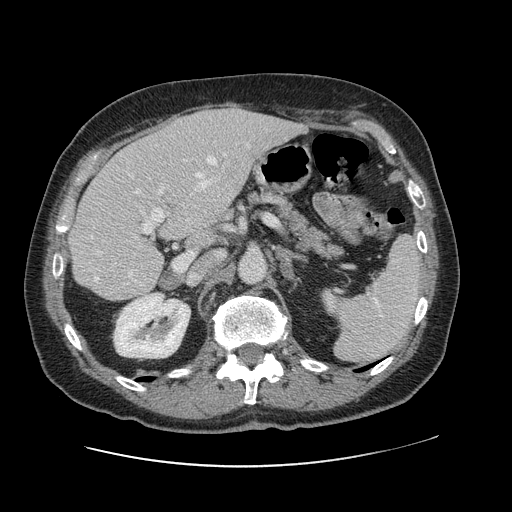
Contrast-enhanced abdominal CT, one axial slice; slice 64 of 138 in the series (ordered by position); 120 kVp; intravenous contrast given; soft-tissue window (W 400 / L 40 HU); 512 × 512 image matrix, field of view 402 × 402 mm. Male patient, age 71 years. From the clinical record (not read from this slice): diagnosis: colorectal cancer liver metastases, imaged before liver resection; multiple liver metastases: no.
Outlined on this slice (outlined manually by an expert reader):
- hepatic veins: box from (x=91, y=158) to (x=227, y=282) px
- liver: (x=71, y=107)–(x=300, y=300)
- planned liver remnant (the part of the liver to remain after resection): (x=71, y=144)–(x=211, y=300)
- portal vein (with intrahepatic branches): (x=97, y=144)–(x=249, y=254)